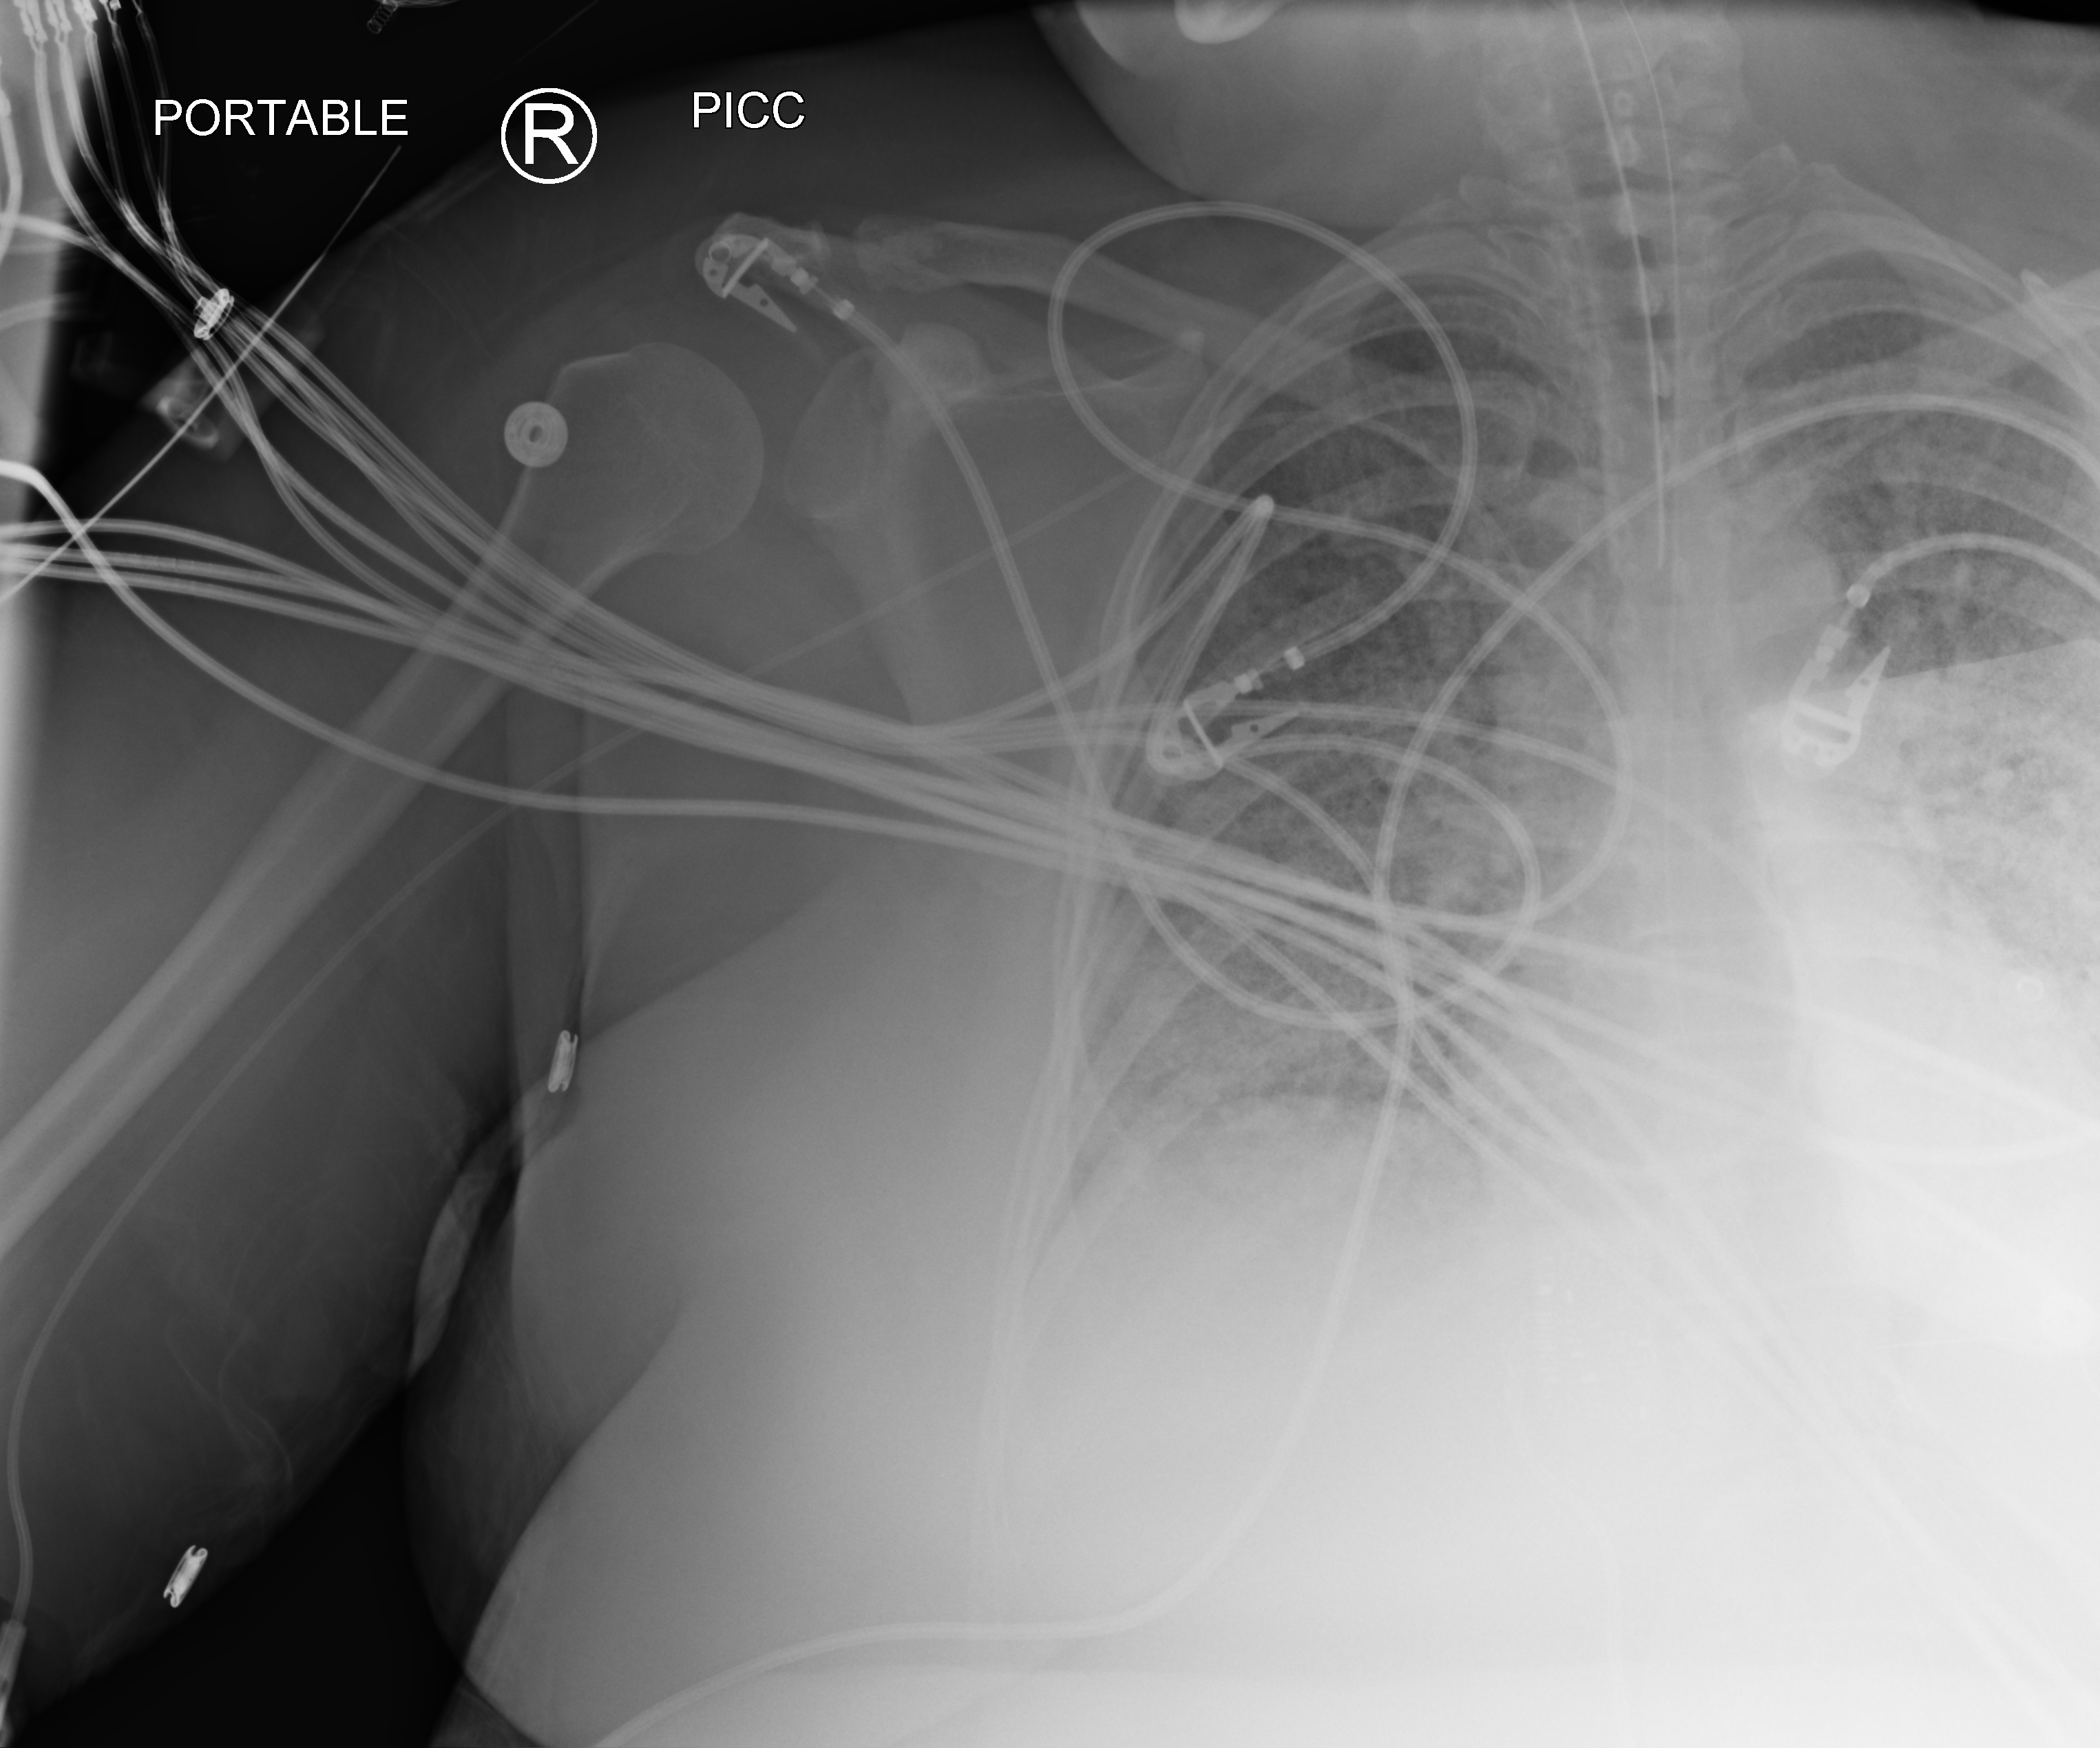
Portable chest radiograph; anteroposterior (AP) projection. Female patient hospitalised with COVID-19, age 18–59 years.
From the hospital-stay record, not from the radiograph (when in the stay this image was taken is not recorded): mechanically ventilated during this hospital stay: yes.